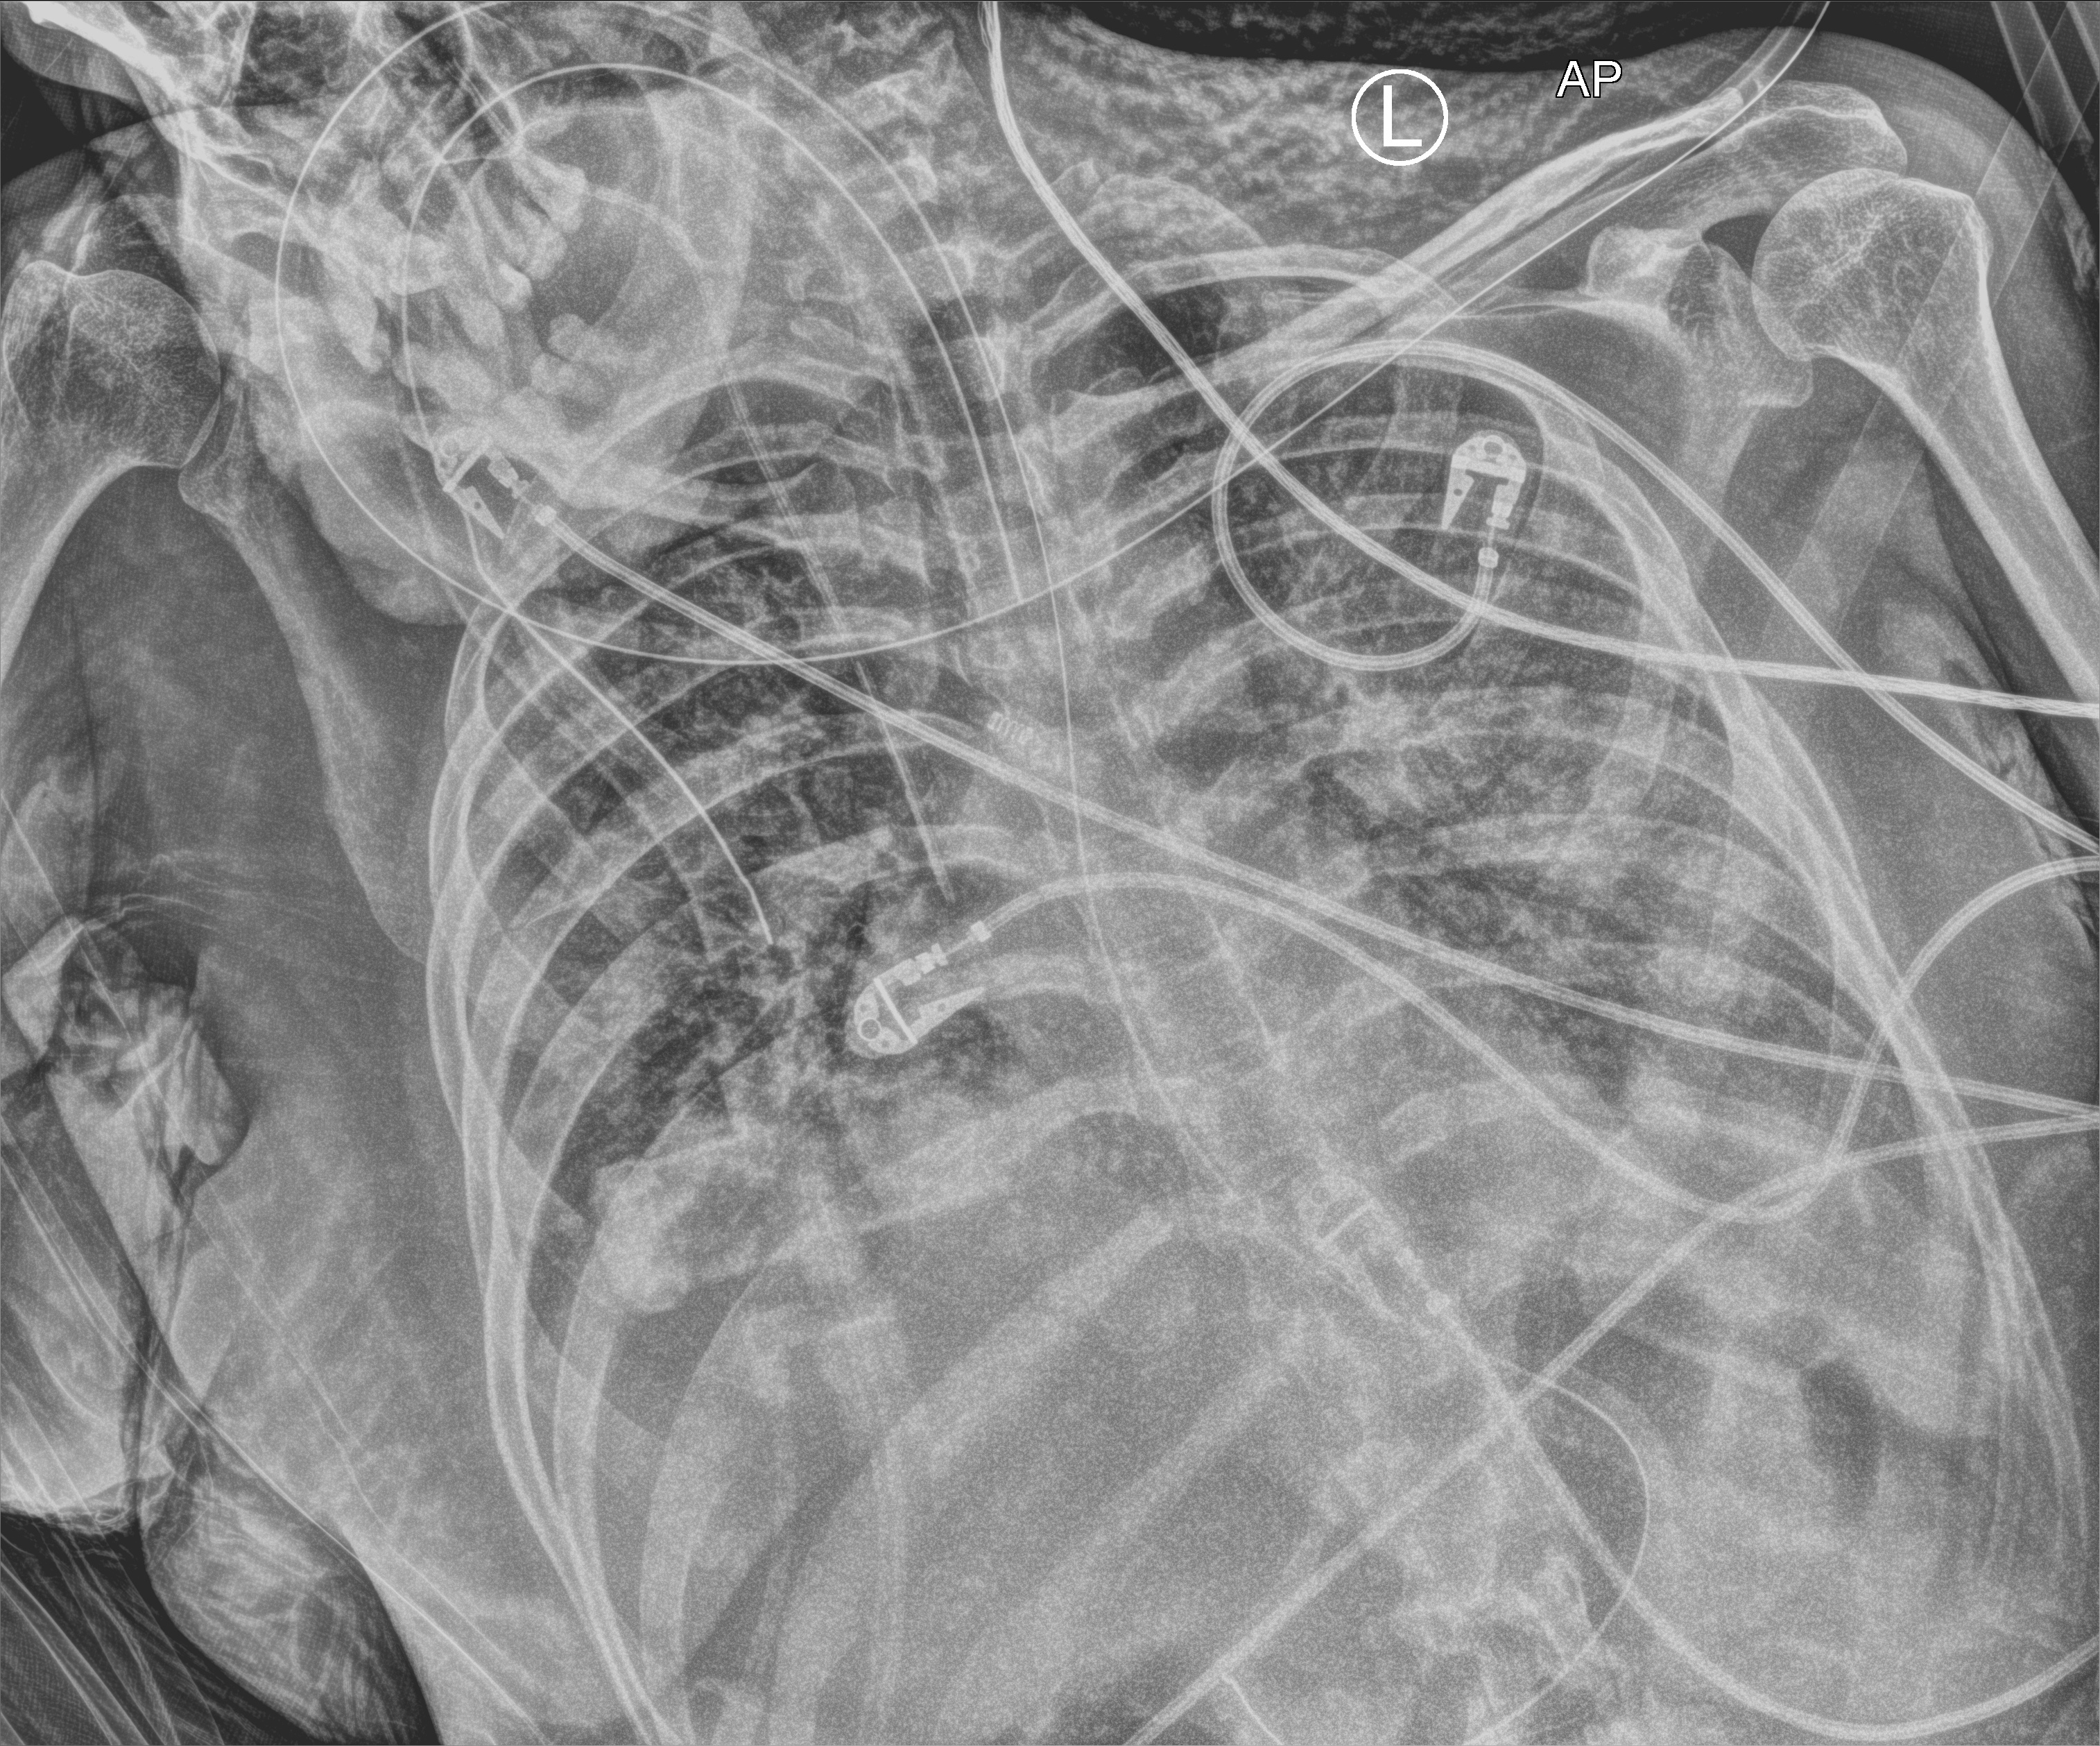
Portable chest radiograph, anteroposterior (AP) projection. Patient hospitalised with COVID-19, aged 18–59 years.
Hospital-stay facts (about this admission, not read from this image; timing relative to this image not recorded): other chronic lung disease (admission record): no.